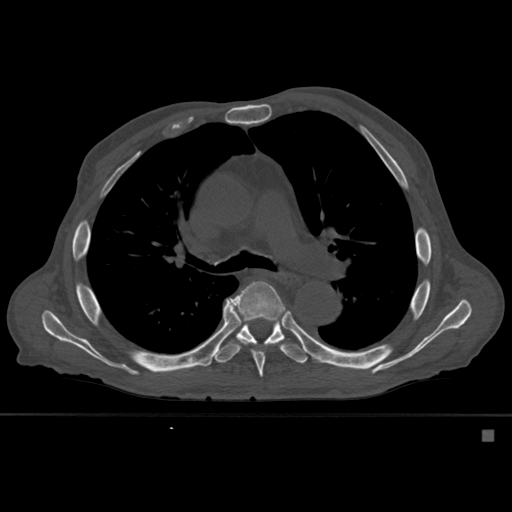
CT including the spine, one axial slice. Slice 377 of 527 in the series (ordered by position). Bone window (W 1800 / L 400 HU). 1.5 mm slice thickness. 512 × 512 image matrix, field of view 373 × 373 mm. Male patient, age 78 years. Case-level facts recorded for this patient, not image findings: primary cancer: prostate.
Structures marked on this image (semi-automatically segmented with operator editing):
- T6 vertebra: box from (x=227, y=280) to (x=288, y=378) px
- T7 vertebra: (x=213, y=317)–(x=309, y=364)